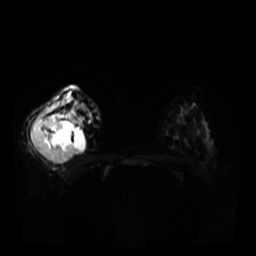
Breast MRI, one axial slice. Position 20 of 34 along the scan axis. Diffusion-weighted series; image 2 of 4 stored at this slice position (different b-values; order by instance number). 3 T. 256 × 256 image matrix, field of view 320 × 320 mm. Female patient.
Outlined on this slice (manually delineated by an expert):
- tumour on diffusion-weighted imaging: bounding box [x1, y1, x2, y2] px = [32, 120, 76, 164]